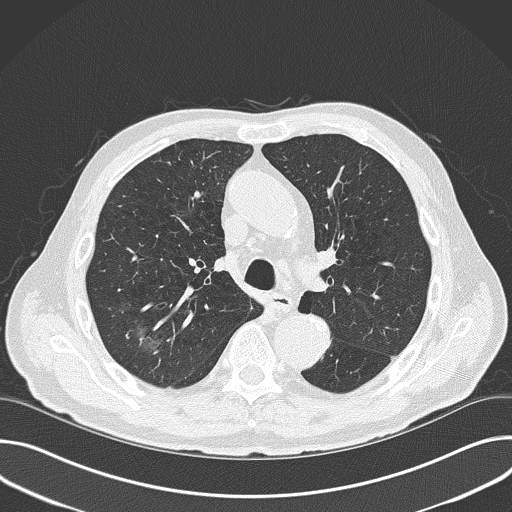
Chest CT (low-dose screening protocol), one axial image, baseline annual screen, lung window (W 1500 / L -600 HU), 2 mm slice thickness, lung (sharp) reconstruction kernel (B50f), slice 111 of 177 in the series. Male, age 74 years at enrolment. Former smoker at enrolment.
- Expert reader's lesion annotation, bounding box <124,313,180,366> (left, top, right, bottom; pixels).
- The screening reader recorded 3 non-calcified nodules or masses ≥4 mm on this exam (right upper lobe, right upper lobe, right middle lobe); which of them this box marks is not recorded.
- Official screen result: positive, change unspecified: nodule(s) >= 4 mm or enlarging nodule(s), mass(es), or other non-specific abnormalities suspicious for lung cancer.
- Participant outcome: lung cancer diagnosed 215 days after this screen — small cell carcinoma, NOS, right upper lobe, stage IV (AJCC 6th edition), 15 mm at pathology.